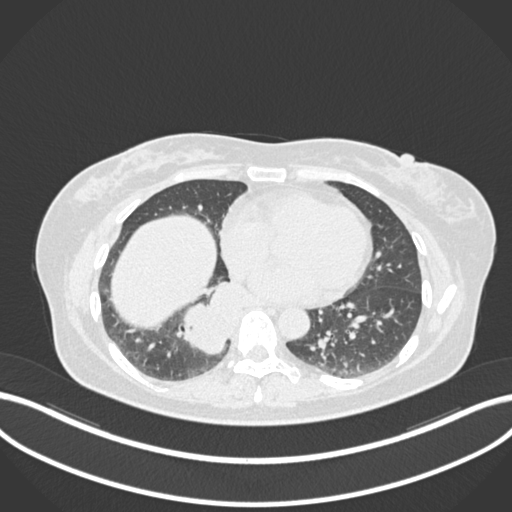
Chest CT, one axial slice; slice 557 of 677 in the series (ordered by position); reconstruction kernel B30f; 120 kVp; lung window (W 1500 / L -600 HU); 1 mm slice thickness; 512 × 512 image matrix. Female patient, age 54 years. From the clinical record (not read from this slice): clinical TNM (as recorded): T4 N0 M0.
Outlined on this slice (rectangle marked by the reading radiologist):
- lung tumour (recorded histology: adenocarcinoma): bounding box <176,281,243,360> (left, top, right, bottom; pixels)